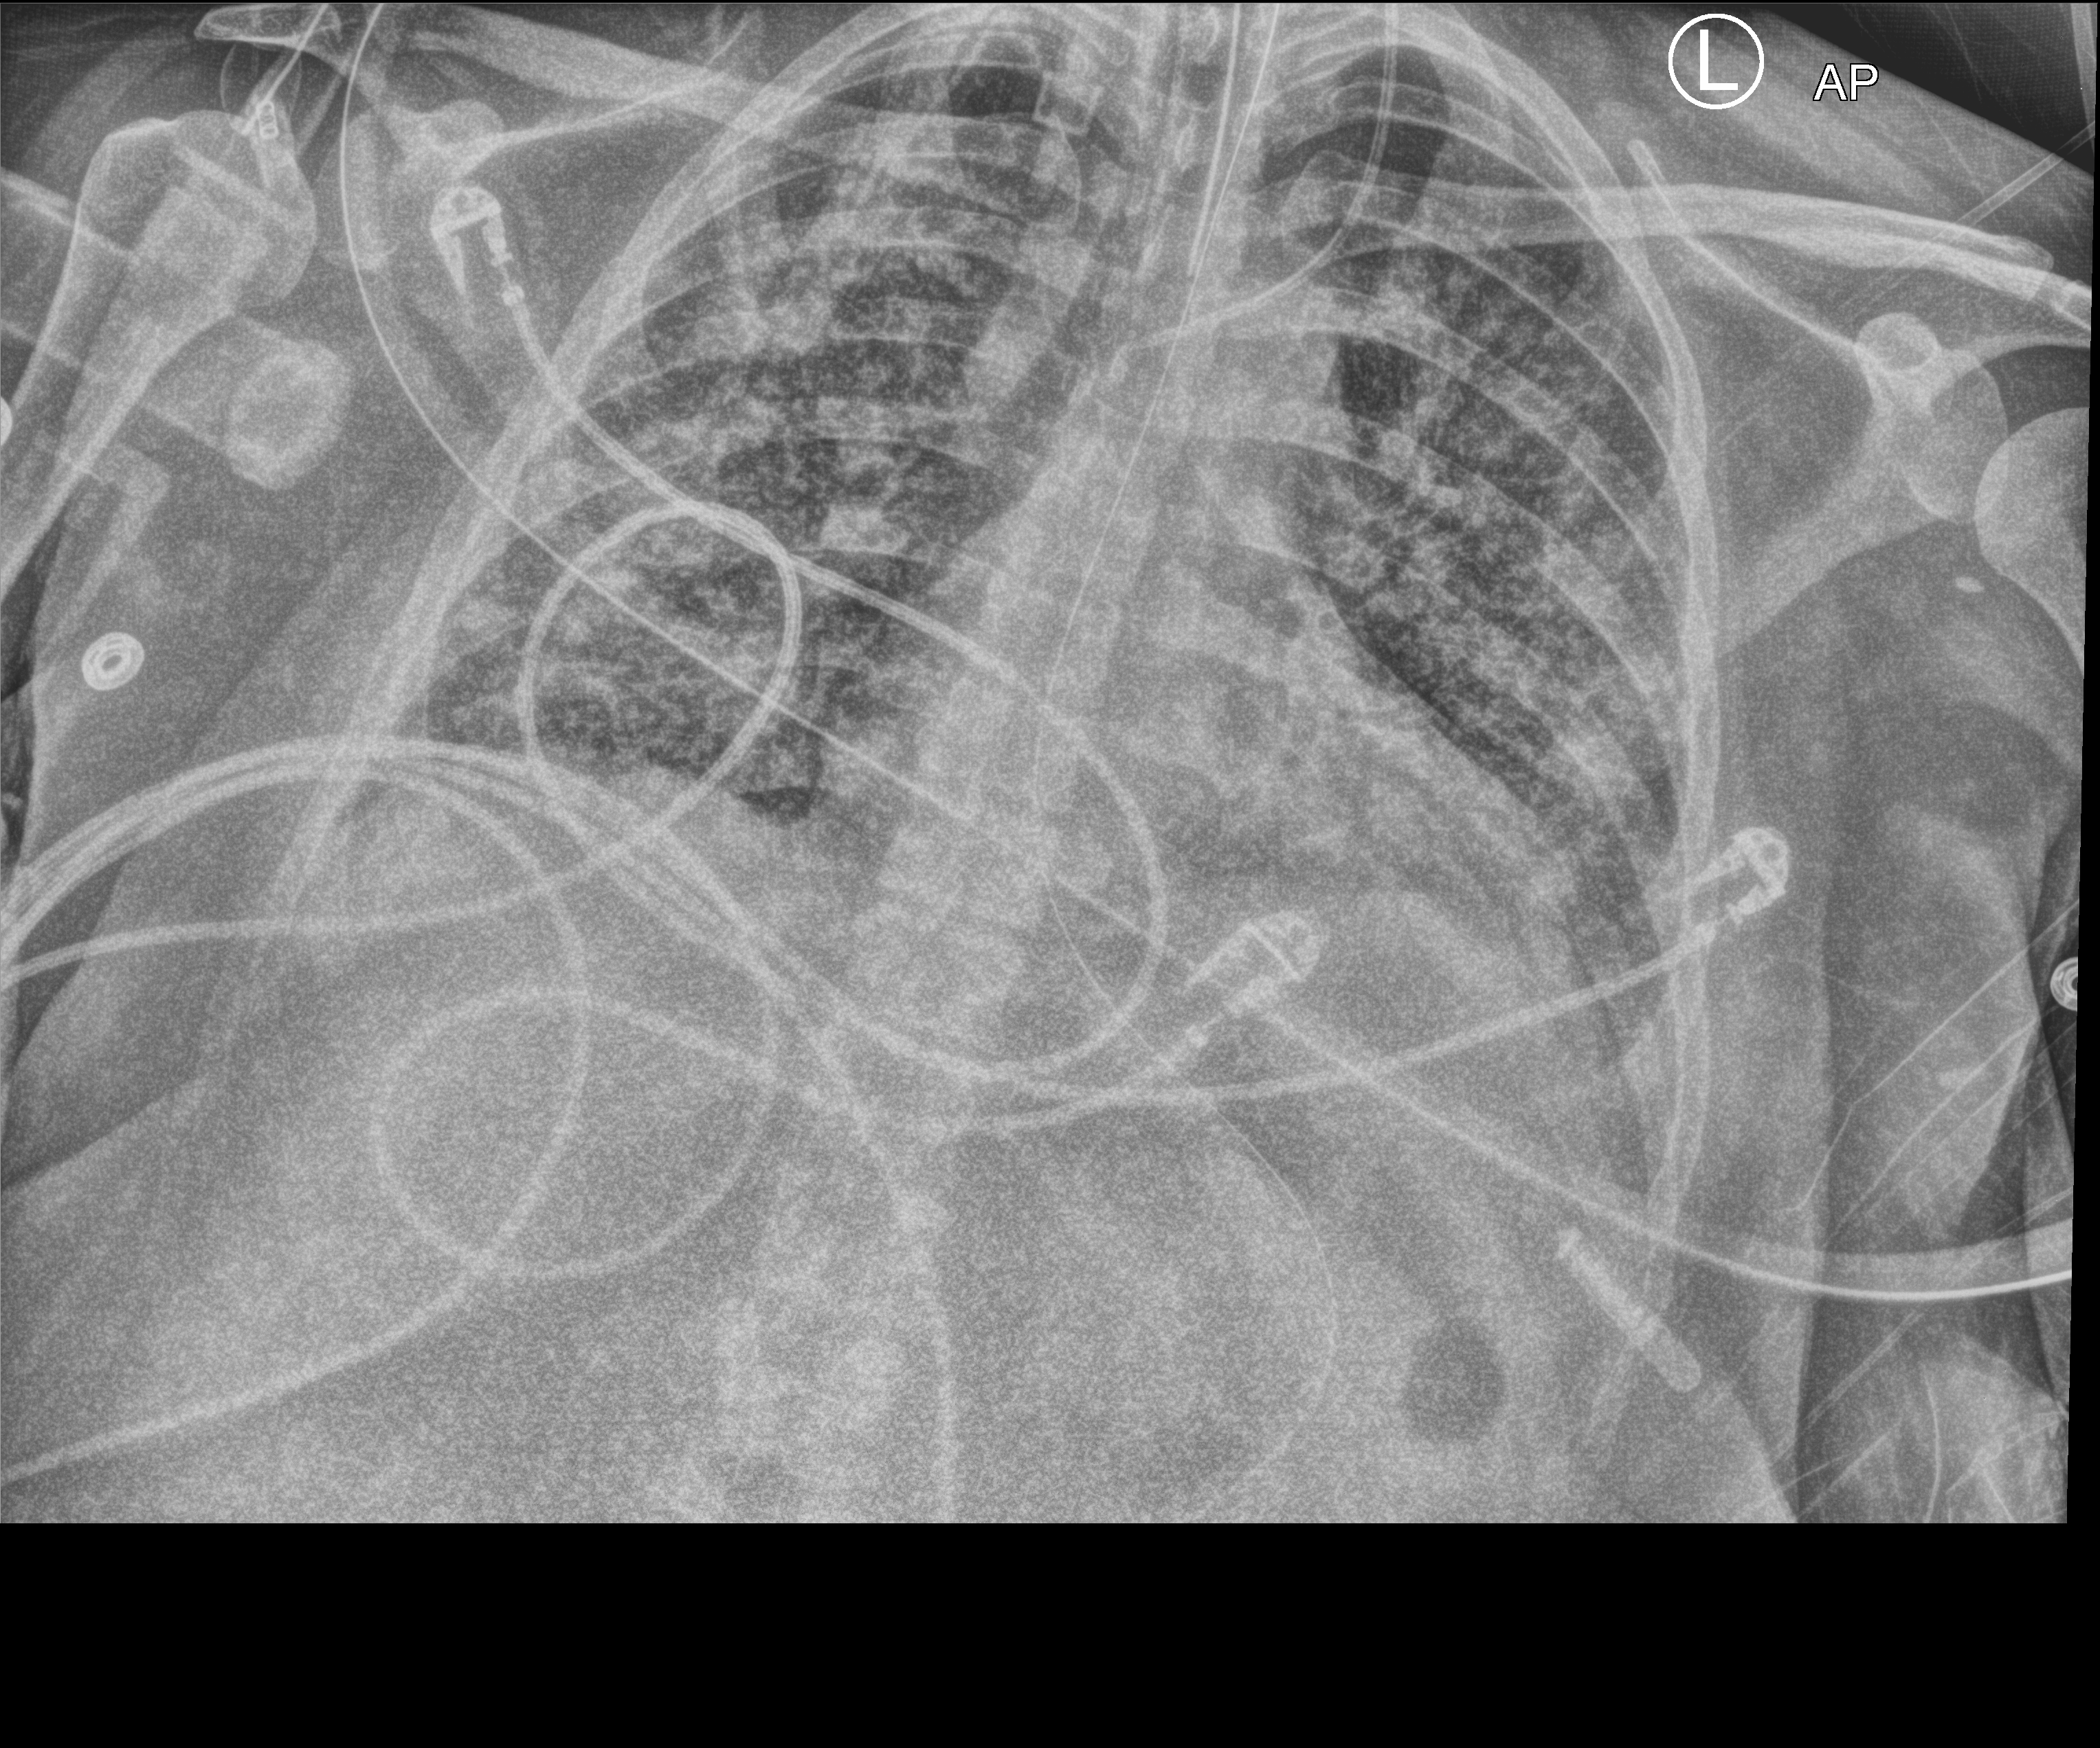
Bedside chest radiograph (computed radiography); anteroposterior (AP) projection. Patient hospitalised with COVID-19; female, aged 18–59 years.
Admission-level facts for this patient (not findings on this image; timing relative to this image not recorded):
- admitted to intensive care during this hospital stay: no